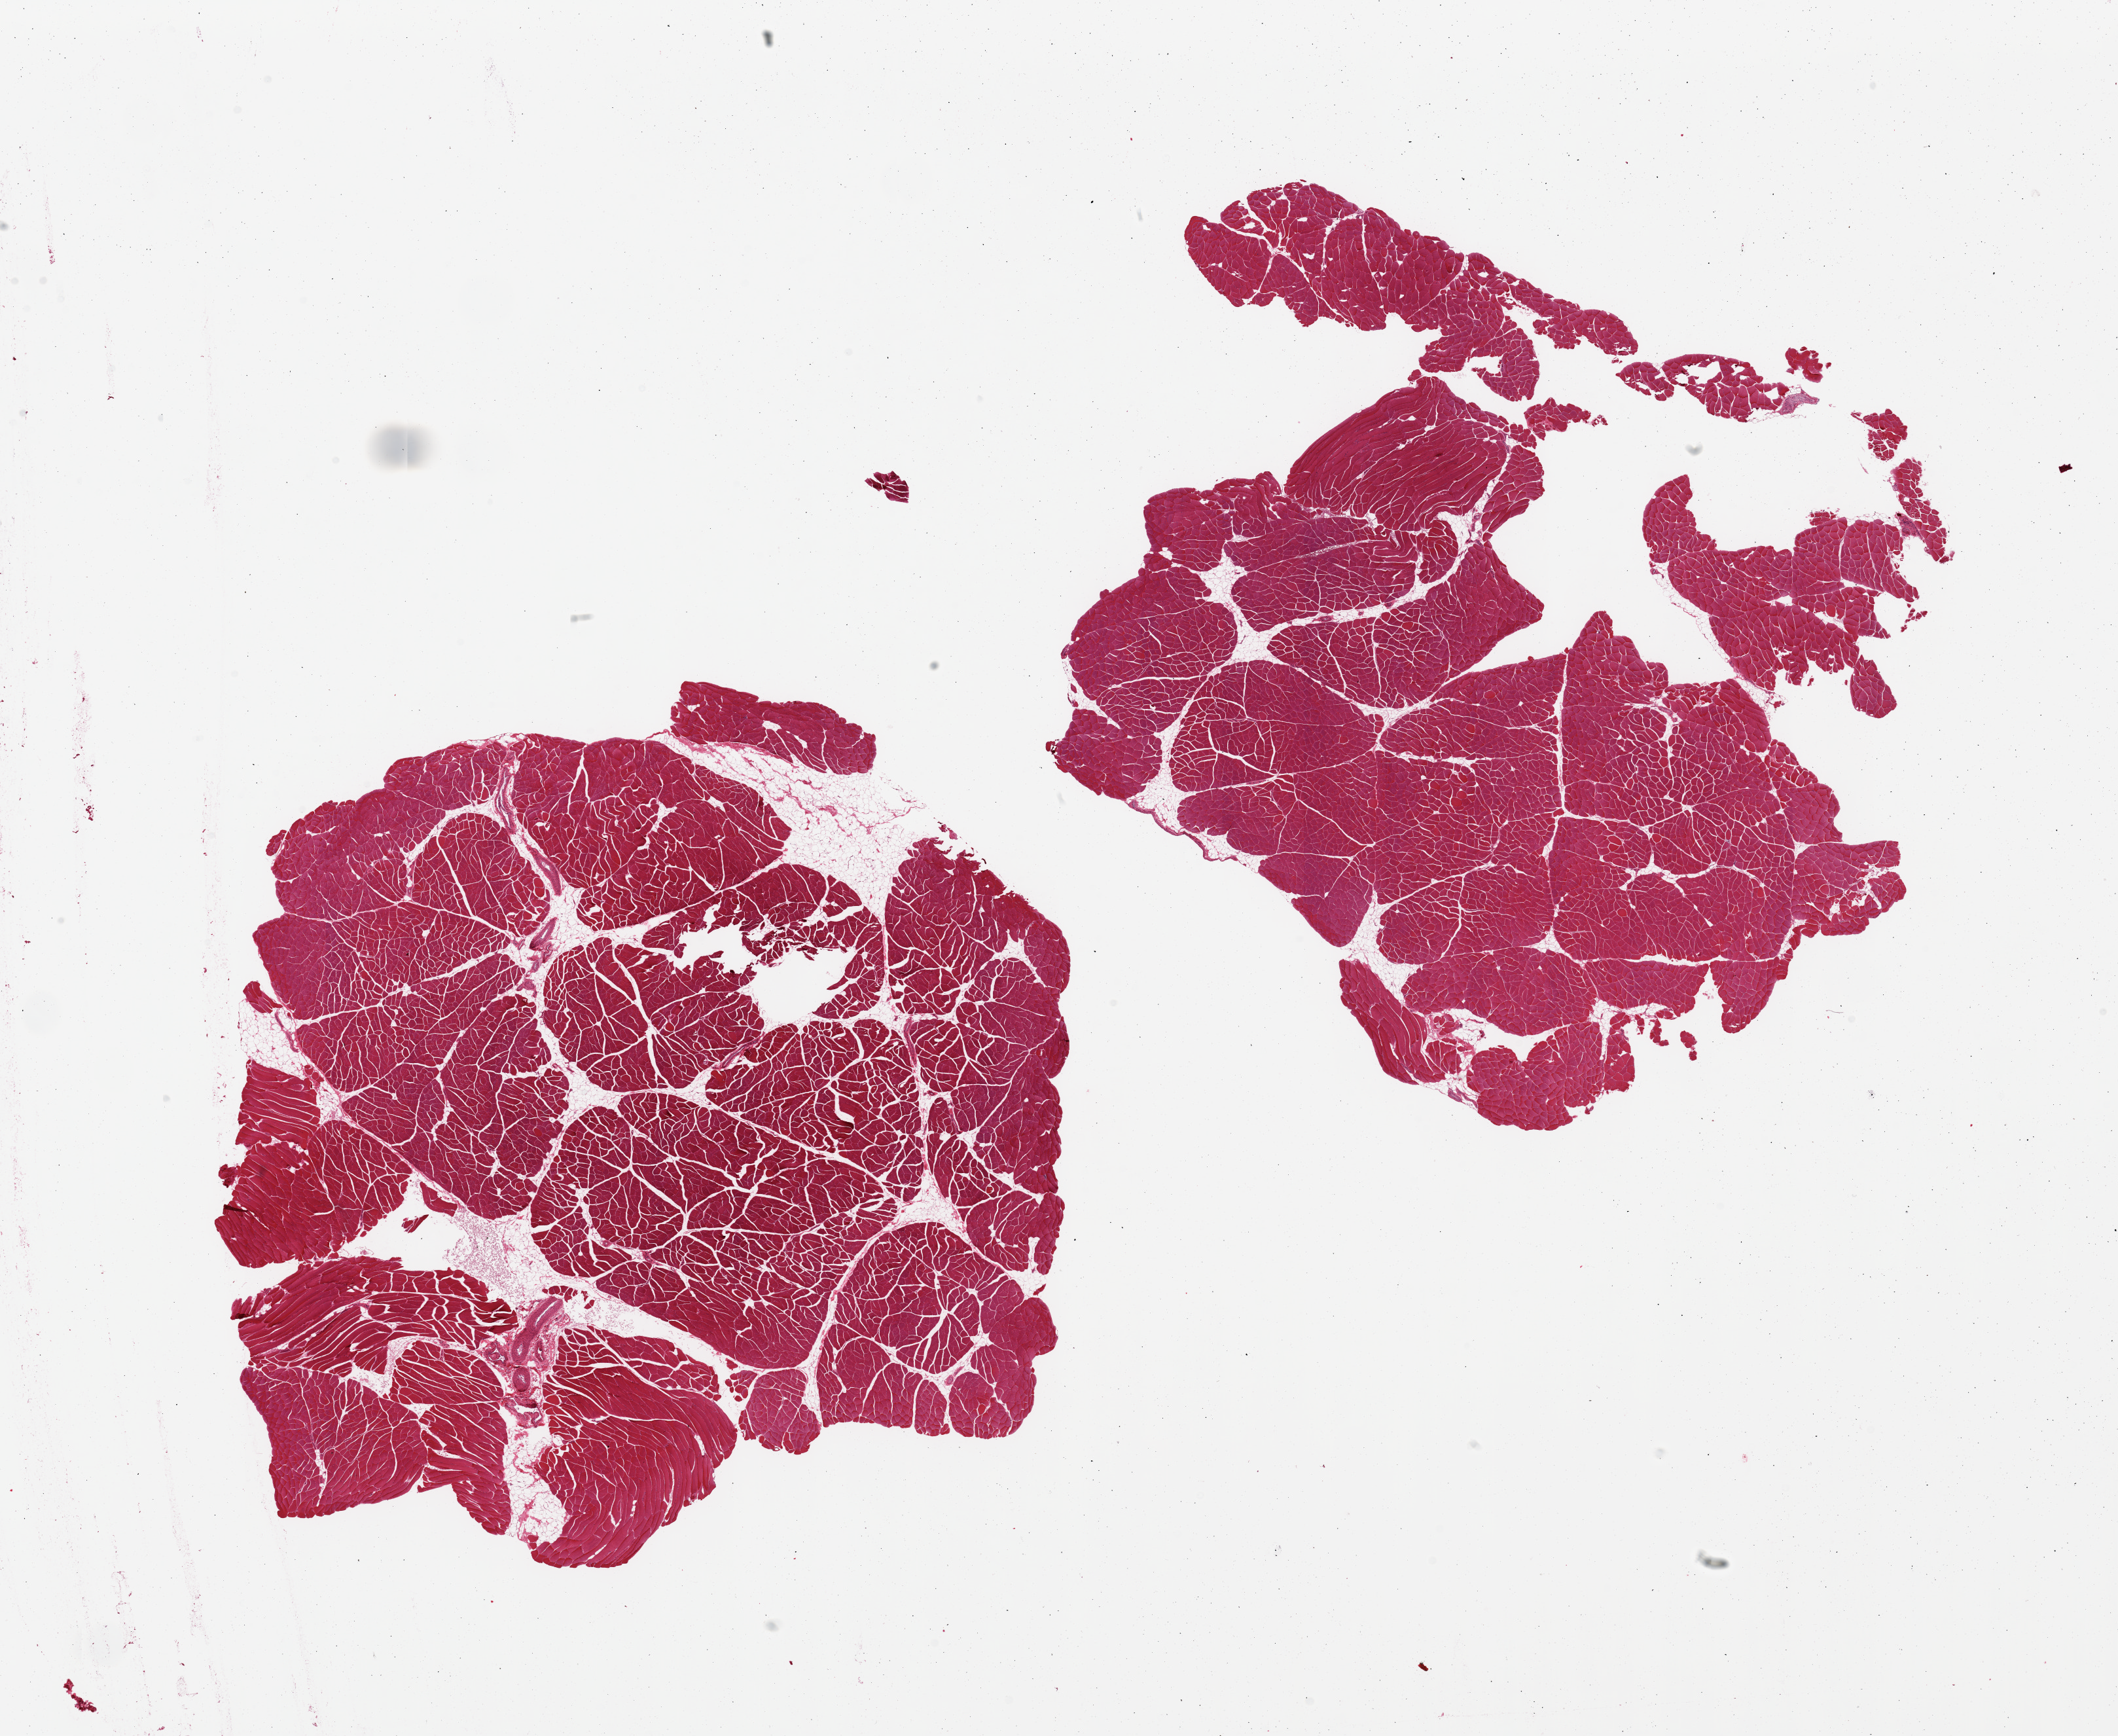
Digitized H&E-stained section, brightfield, low-resolution overview of the scanned area, about 25.6 x 21.0 mm (slide scanned at 20x), PAXgene-fixed, paraffin-embedded tissue, sampled site (target tissue): skeletal muscle, tissue donor sample. Female donor.
Pathologist's review note for this sample: 2 pieces, trace-minimal interstitial fat.